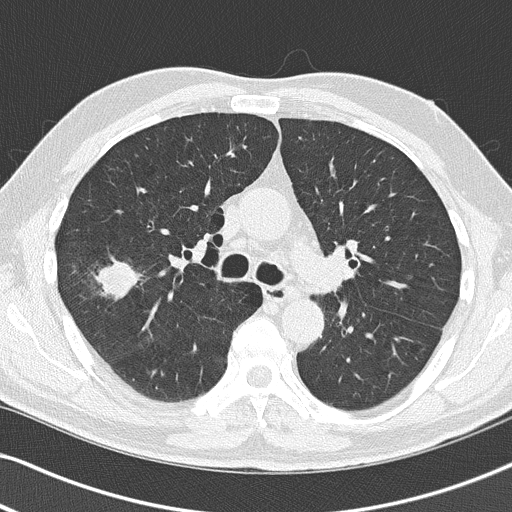
Low-dose screening chest CT, one axial slice; slice 83 of 140 in the series (ordered by position); reconstruction kernel B50f; 120 kVp; lung window (W 1500 / L -600 HU); 2 mm slice thickness; 512 × 512 image matrix, field of view 330 × 330 mm.
Structures marked on this image (manually delineated by an expert):
- lesion 1 (tumor, upper lobe of right lung): bounding box (x1, y1, x2, y2) in pixels: (96, 261, 140, 298)